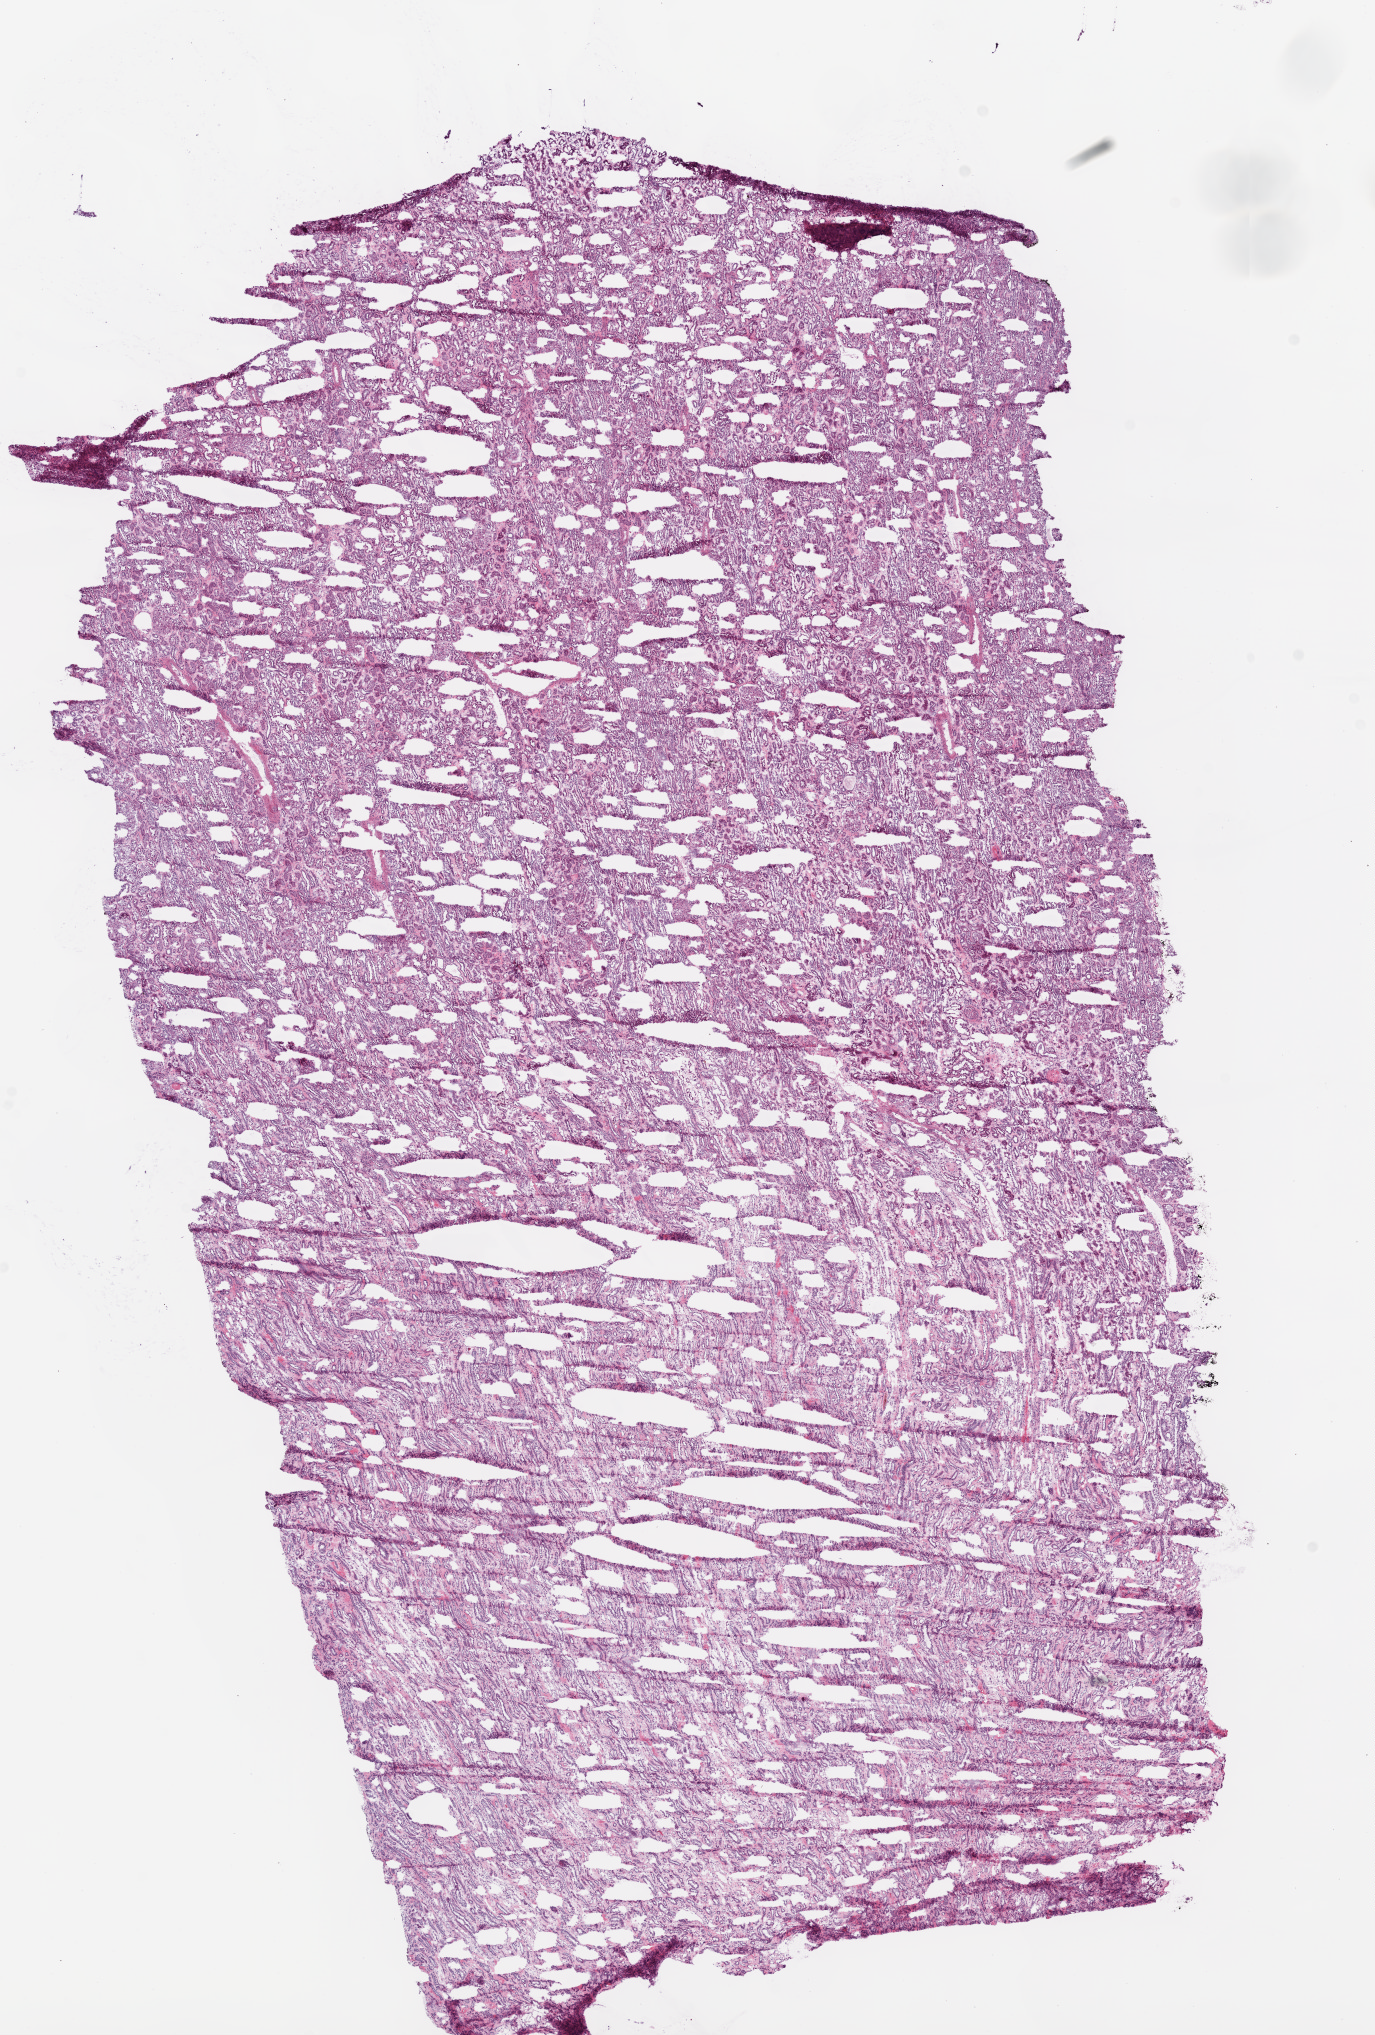
Hematoxylin and eosin (H&E) stained whole-slide image, whole scanned area (about 11.0 x 16.3 mm, from a 20x scan) shown as a low-resolution overview. Frozen section from the top of the tissue portion. Kidney, solid tissue normal (non-tumour tissue) sample. Male patient; age at initial diagnosis 52 years.
• this section: solid tissue normal (non-tumour) sample from the same patient
• patient diagnosis: Clear cell adenocarcinoma, NOS